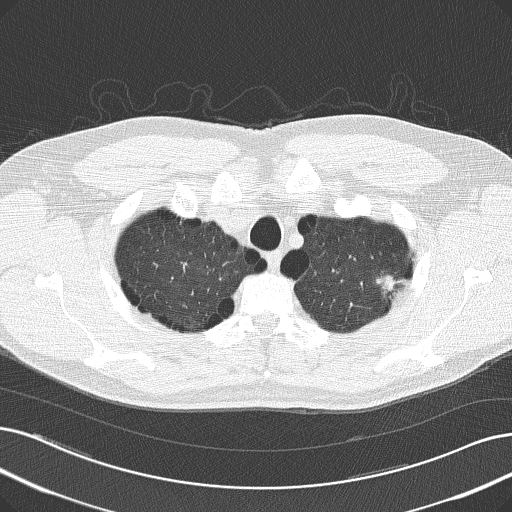
Axial slice from a low-dose chest CT screening exam. First (baseline) screen. Lung window (W 1500 / L -600 HU). Lung (sharp) reconstruction kernel (B50f). 120 kVp. Slice 34 of 181 in the series. 512 × 512 image matrix. Male participant, aged 62 years at enrolment. Current smoker at enrolment.
- Expert reader's lesion annotation, bounding box <359,257,412,308> (left, top, right, bottom; pixels).
- The screening reader recorded 4 non-calcified nodules or masses ≥4 mm on this exam (left upper lobe, right upper lobe, right upper lobe, right middle lobe); which of them this box marks is not recorded.
- Later outcome: lung cancer diagnosed 383 days after this screen — adenocarcinoma, NOS, left upper lobe, well differentiated (G1), stage IB (AJCC 6th edition), 17 mm at pathology.